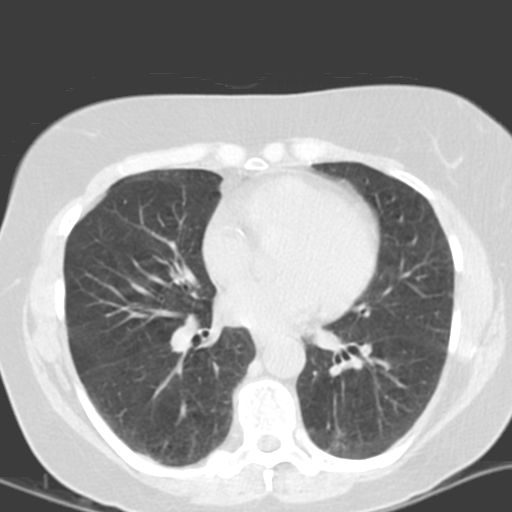
Low-dose screening chest CT, axial slice. Second annual screen. Lung window (W 1500 / L -600 HU). 3.2 mm slice thickness. Standard (soft-tissue) reconstruction kernel (B). Female participant, aged 55 years at enrolment.
Lesion marked by an expert reader, bounding box (x1, y1, x2, y2) in pixels: (305, 411, 377, 465). The screening reader recorded 4 non-calcified nodules or masses ≥4 mm on this exam (left lower lobe, left lower lobe, left upper lobe, right middle lobe); which of them this box marks is not recorded. Official screen result: positive, other.